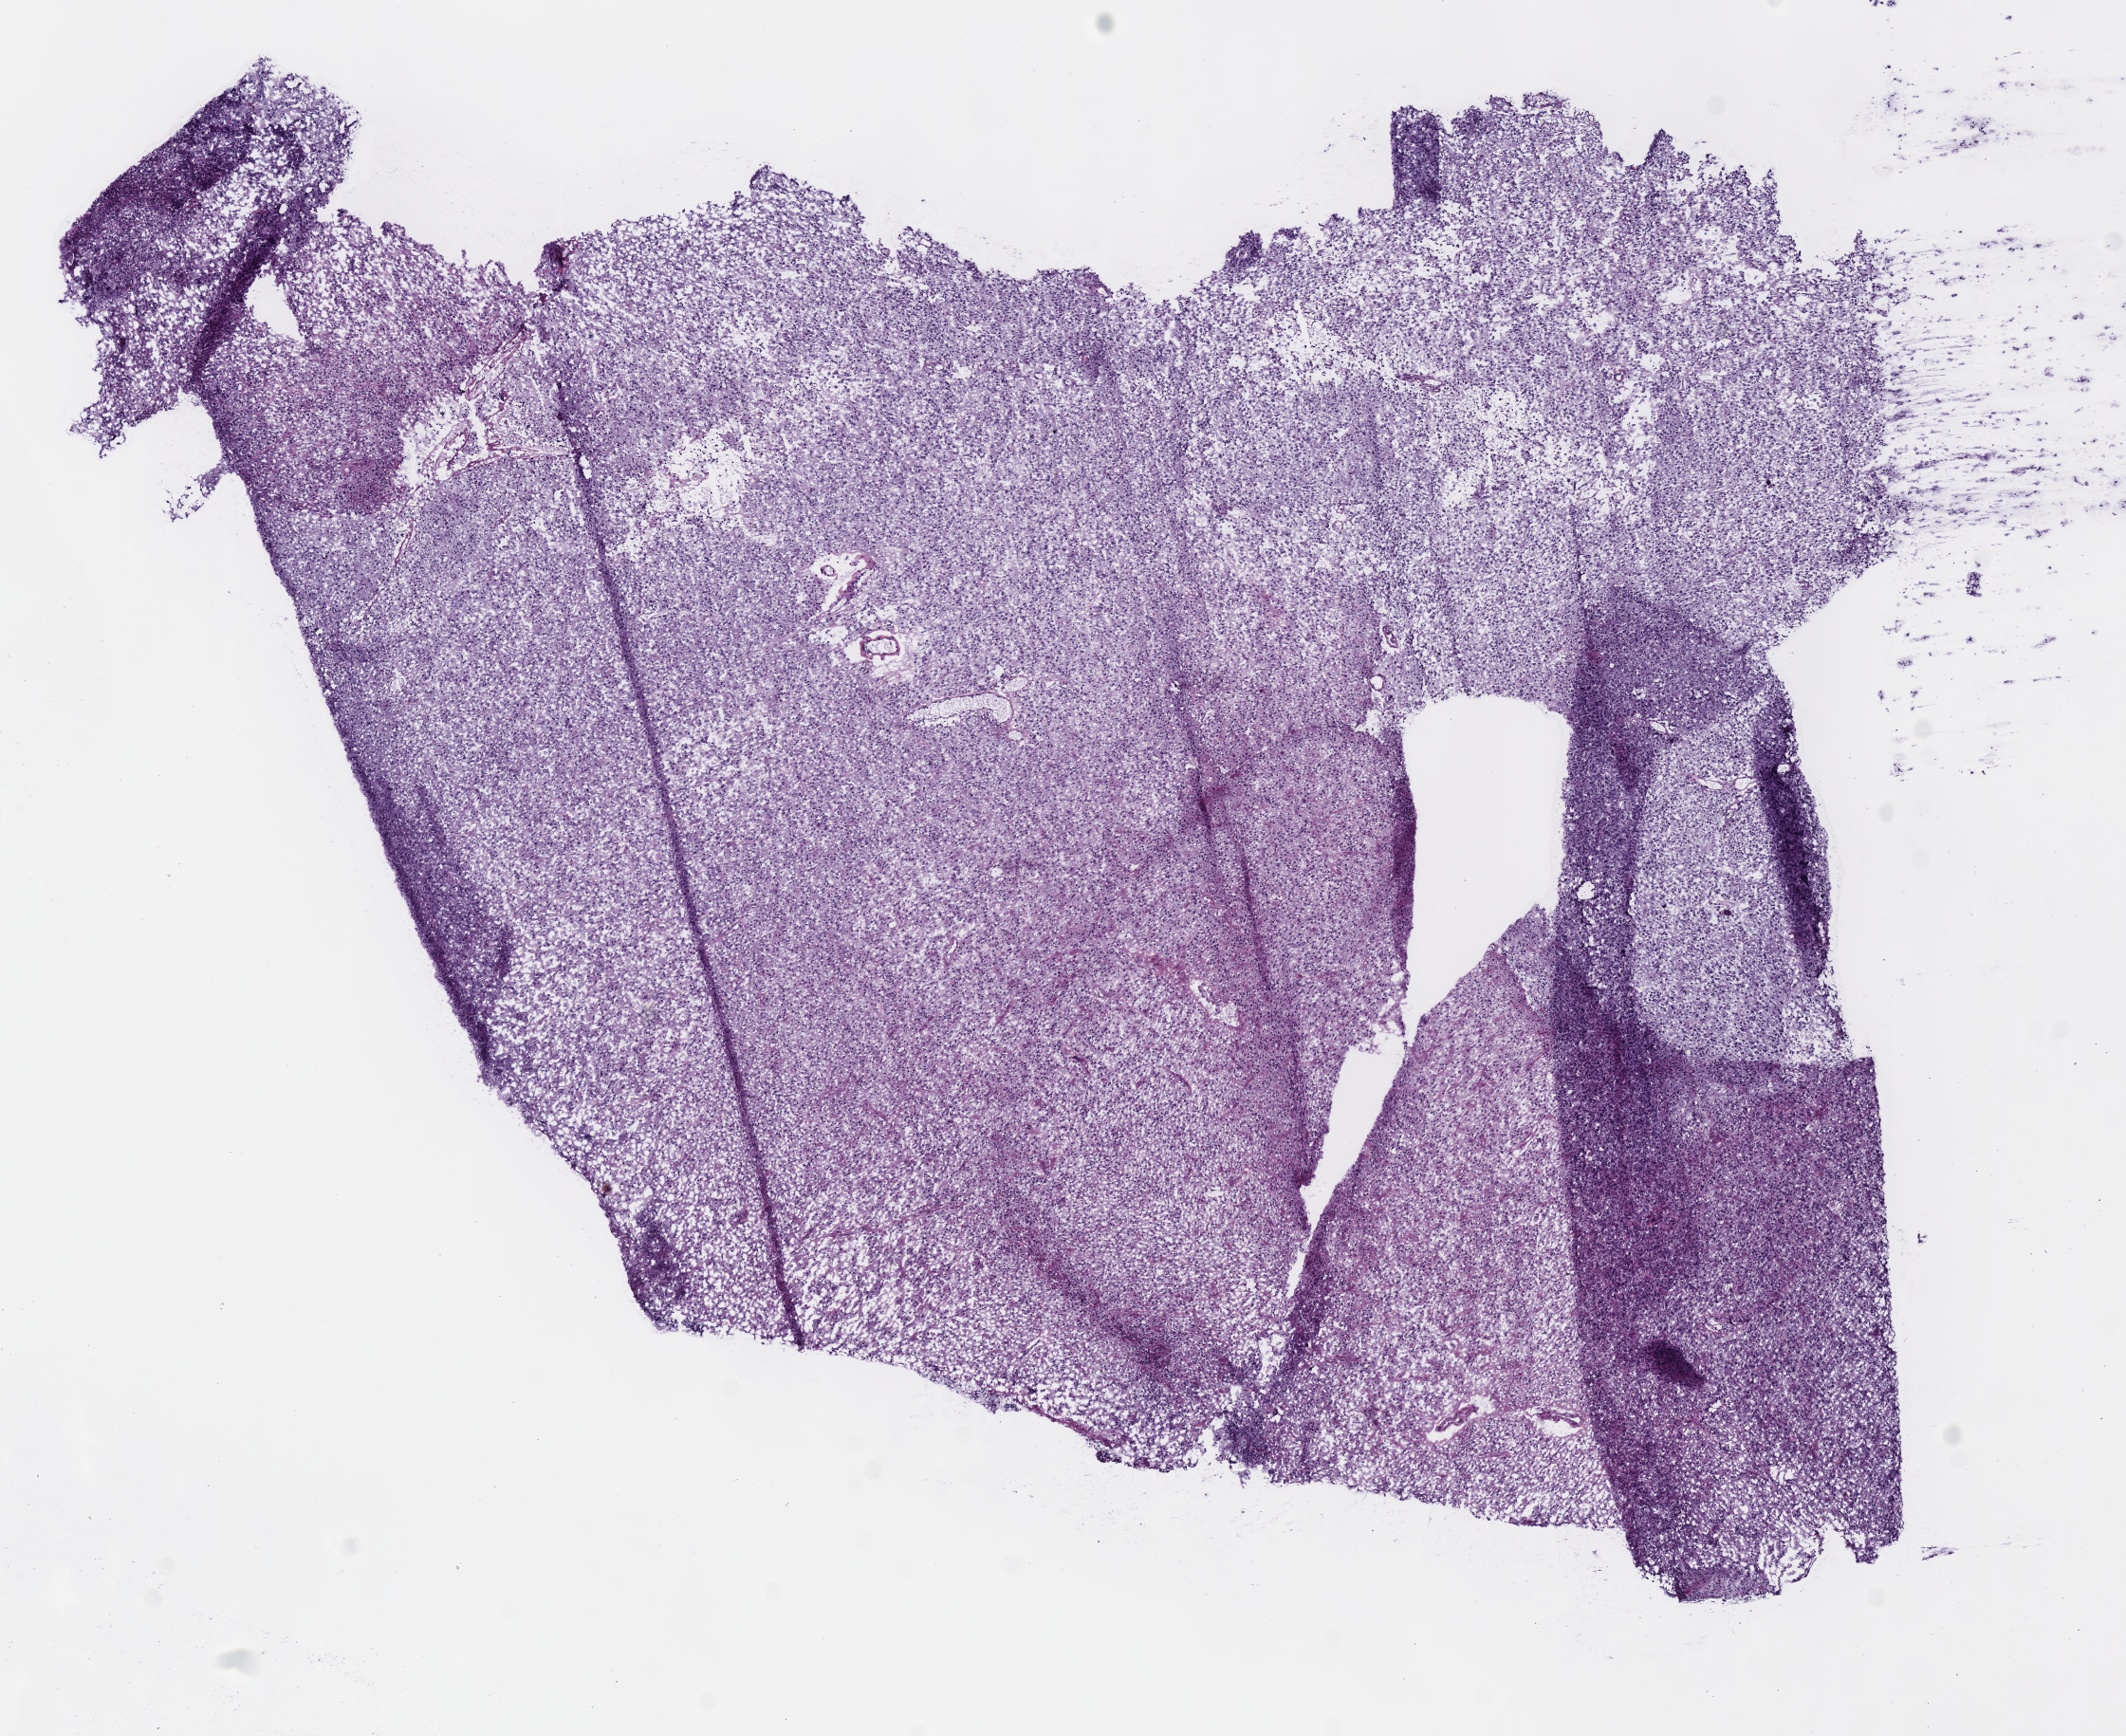
Hematoxylin and eosin (H&E) stained whole-slide image — low-resolution overview of the scanned area, about 8.8 x 7.2 mm; frozen section from the top of the tissue portion; sample: primary tumour, brain. Patient: female, age at initial diagnosis 30 years. Histologic grade: G2 (moderately differentiated). Pathologist review of this section (percent, as recorded): tumour cells 100%, tumour nuclei 80%, normal cells 0%, stromal cells 0%, necrosis 0%.
Pathologic diagnosis: Oligodendroglioma, NOS.